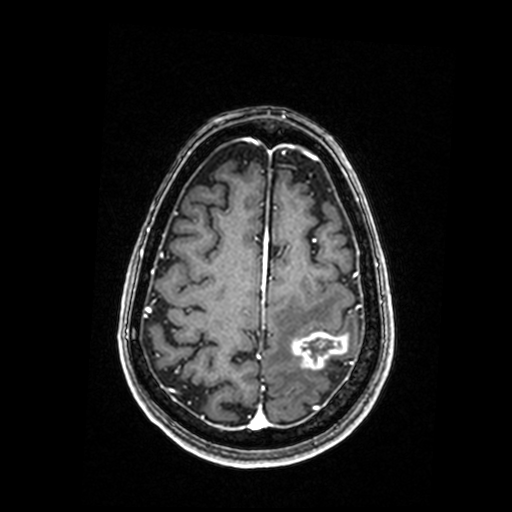
Brain MRI from a brain-tumour surgery series, one axial slice; position 54 of 192 along the scan axis; T1-weighted post-contrast; 0.98 mm slice thickness; 512 × 512 image matrix. From the clinical record (not read from this slice): histopathology: Metastastic Carcinoma, Poorly Differentiated; tumour location: Left Parietal.
Structures marked on this image (manually delineated by an expert):
- tumour: bounding box <292,332,348,369> (left, top, right, bottom; pixels)